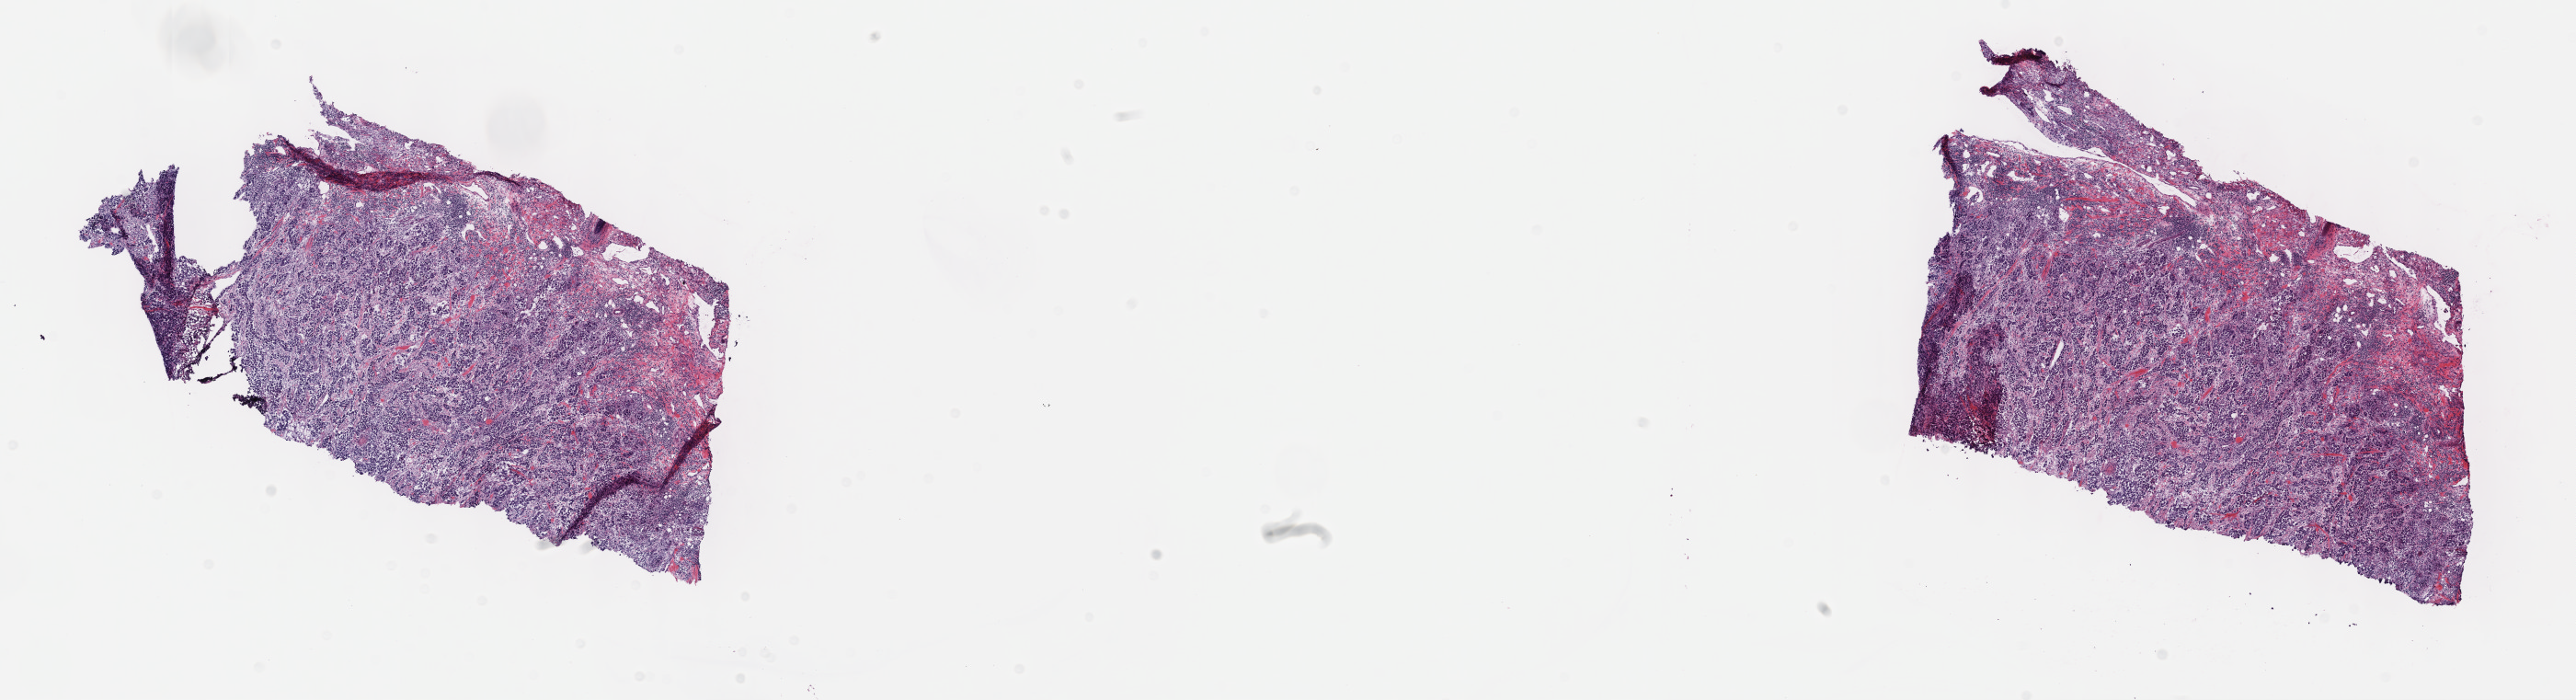
Whole-slide histology image, H&E — whole scanned area (about 22.7 x 6.2 mm) shown as a low-resolution overview, frozen section, head and neck, primary tumour sample. Male patient; age at initial diagnosis 74 years. Histologic grade: G3 (poorly differentiated). Slide review estimates, as recorded: tumour cells 80%, tumour nuclei 80%, normal cells 0%, stromal cells 20%, necrosis 0%. Infiltration values recorded for this section: lymphocyte infiltration 10%, monocyte infiltration 0%, neutrophil infiltration 0%.
AJCC pathologic stage: IVA (7th edition). Diagnosis: Squamous cell carcinoma, NOS (floor of mouth, NOS). Laterality: midline.